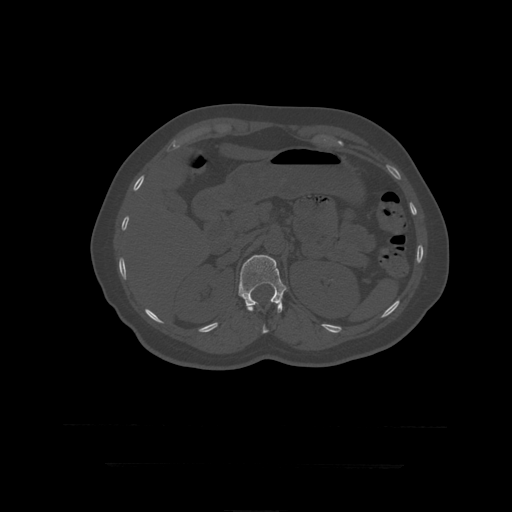
CT including the spine, one axial slice. Slice 182 of 399 in the series (ordered by position). 120 kVp. Bone window (W 1800 / L 400 HU). 1.25 mm slice thickness. 512 × 512 image matrix, field of view 450 × 450 mm. Patient age 41 years. Case-level facts recorded for this patient, not image findings: primary cancer: breast.
Annotated regions visible in this slice (semi-automatic segmentation, software-assisted and operator-edited):
- L1 vertebra: bounding box [x1, y1, x2, y2] px = [239, 255, 286, 313]
- T12 vertebra: [246, 303, 282, 334]